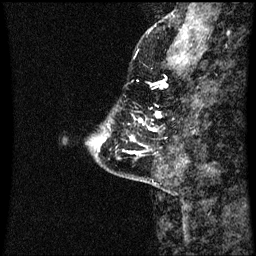
Breast MRI (dynamic contrast-enhanced), one sagittal slice. Dynamic contrast-enhanced series, image 2 of 3 at this slice position (ordered by acquisition). 1.5 T. TE 4.2 ms, TR 8.9 ms. 2 mm slice thickness. 256 × 256 image matrix, field of view 200 × 200 mm. Patient: female, 43 years. Case-level facts recorded for this patient, not image findings: setting: breast cancer imaged before/during neoadjuvant chemotherapy; receptor status: HR-positive, HER2-negative.
Outlined on this slice (semi-automatically segmented with operator editing):
- analysis volume of interest (the breast-tissue region the enhancement analysis was run in; not a lesion): bounding box <123,116,158,153> (left, top, right, bottom; pixels)
- tumour enhancement mask (voxels above the 70 % enhancement threshold inside the analysis volume of interest): <132,128,155,153>